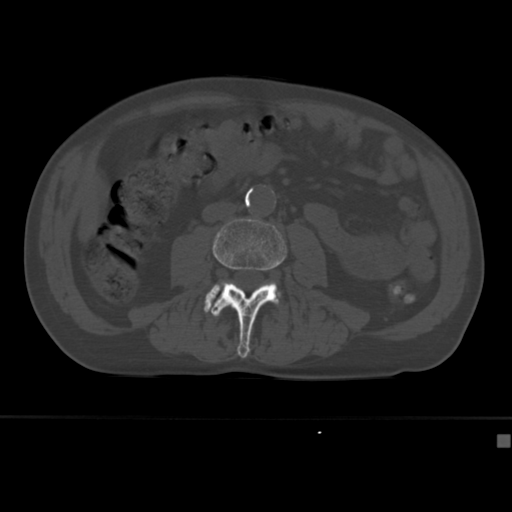
CT including the spine, one axial slice; position 123 of 430 along the scan axis; reconstruction kernel Br40s; 120 kVp; bone window (W 1800 / L 400 HU); 1.5 mm slice thickness; 512 × 512 image matrix. Male patient, age 64 years. Case-level facts recorded for this patient, not image findings: primary cancer: uterus; vertebrae with lytic lesions (as recorded): T1, T4, T5, T7, L5.
Annotated regions visible in this slice (semi-automatically segmented with operator editing):
- L3 vertebra: box from (x=211, y=218) to (x=287, y=358) px
- L4 vertebra: (x=204, y=285)–(x=279, y=313)